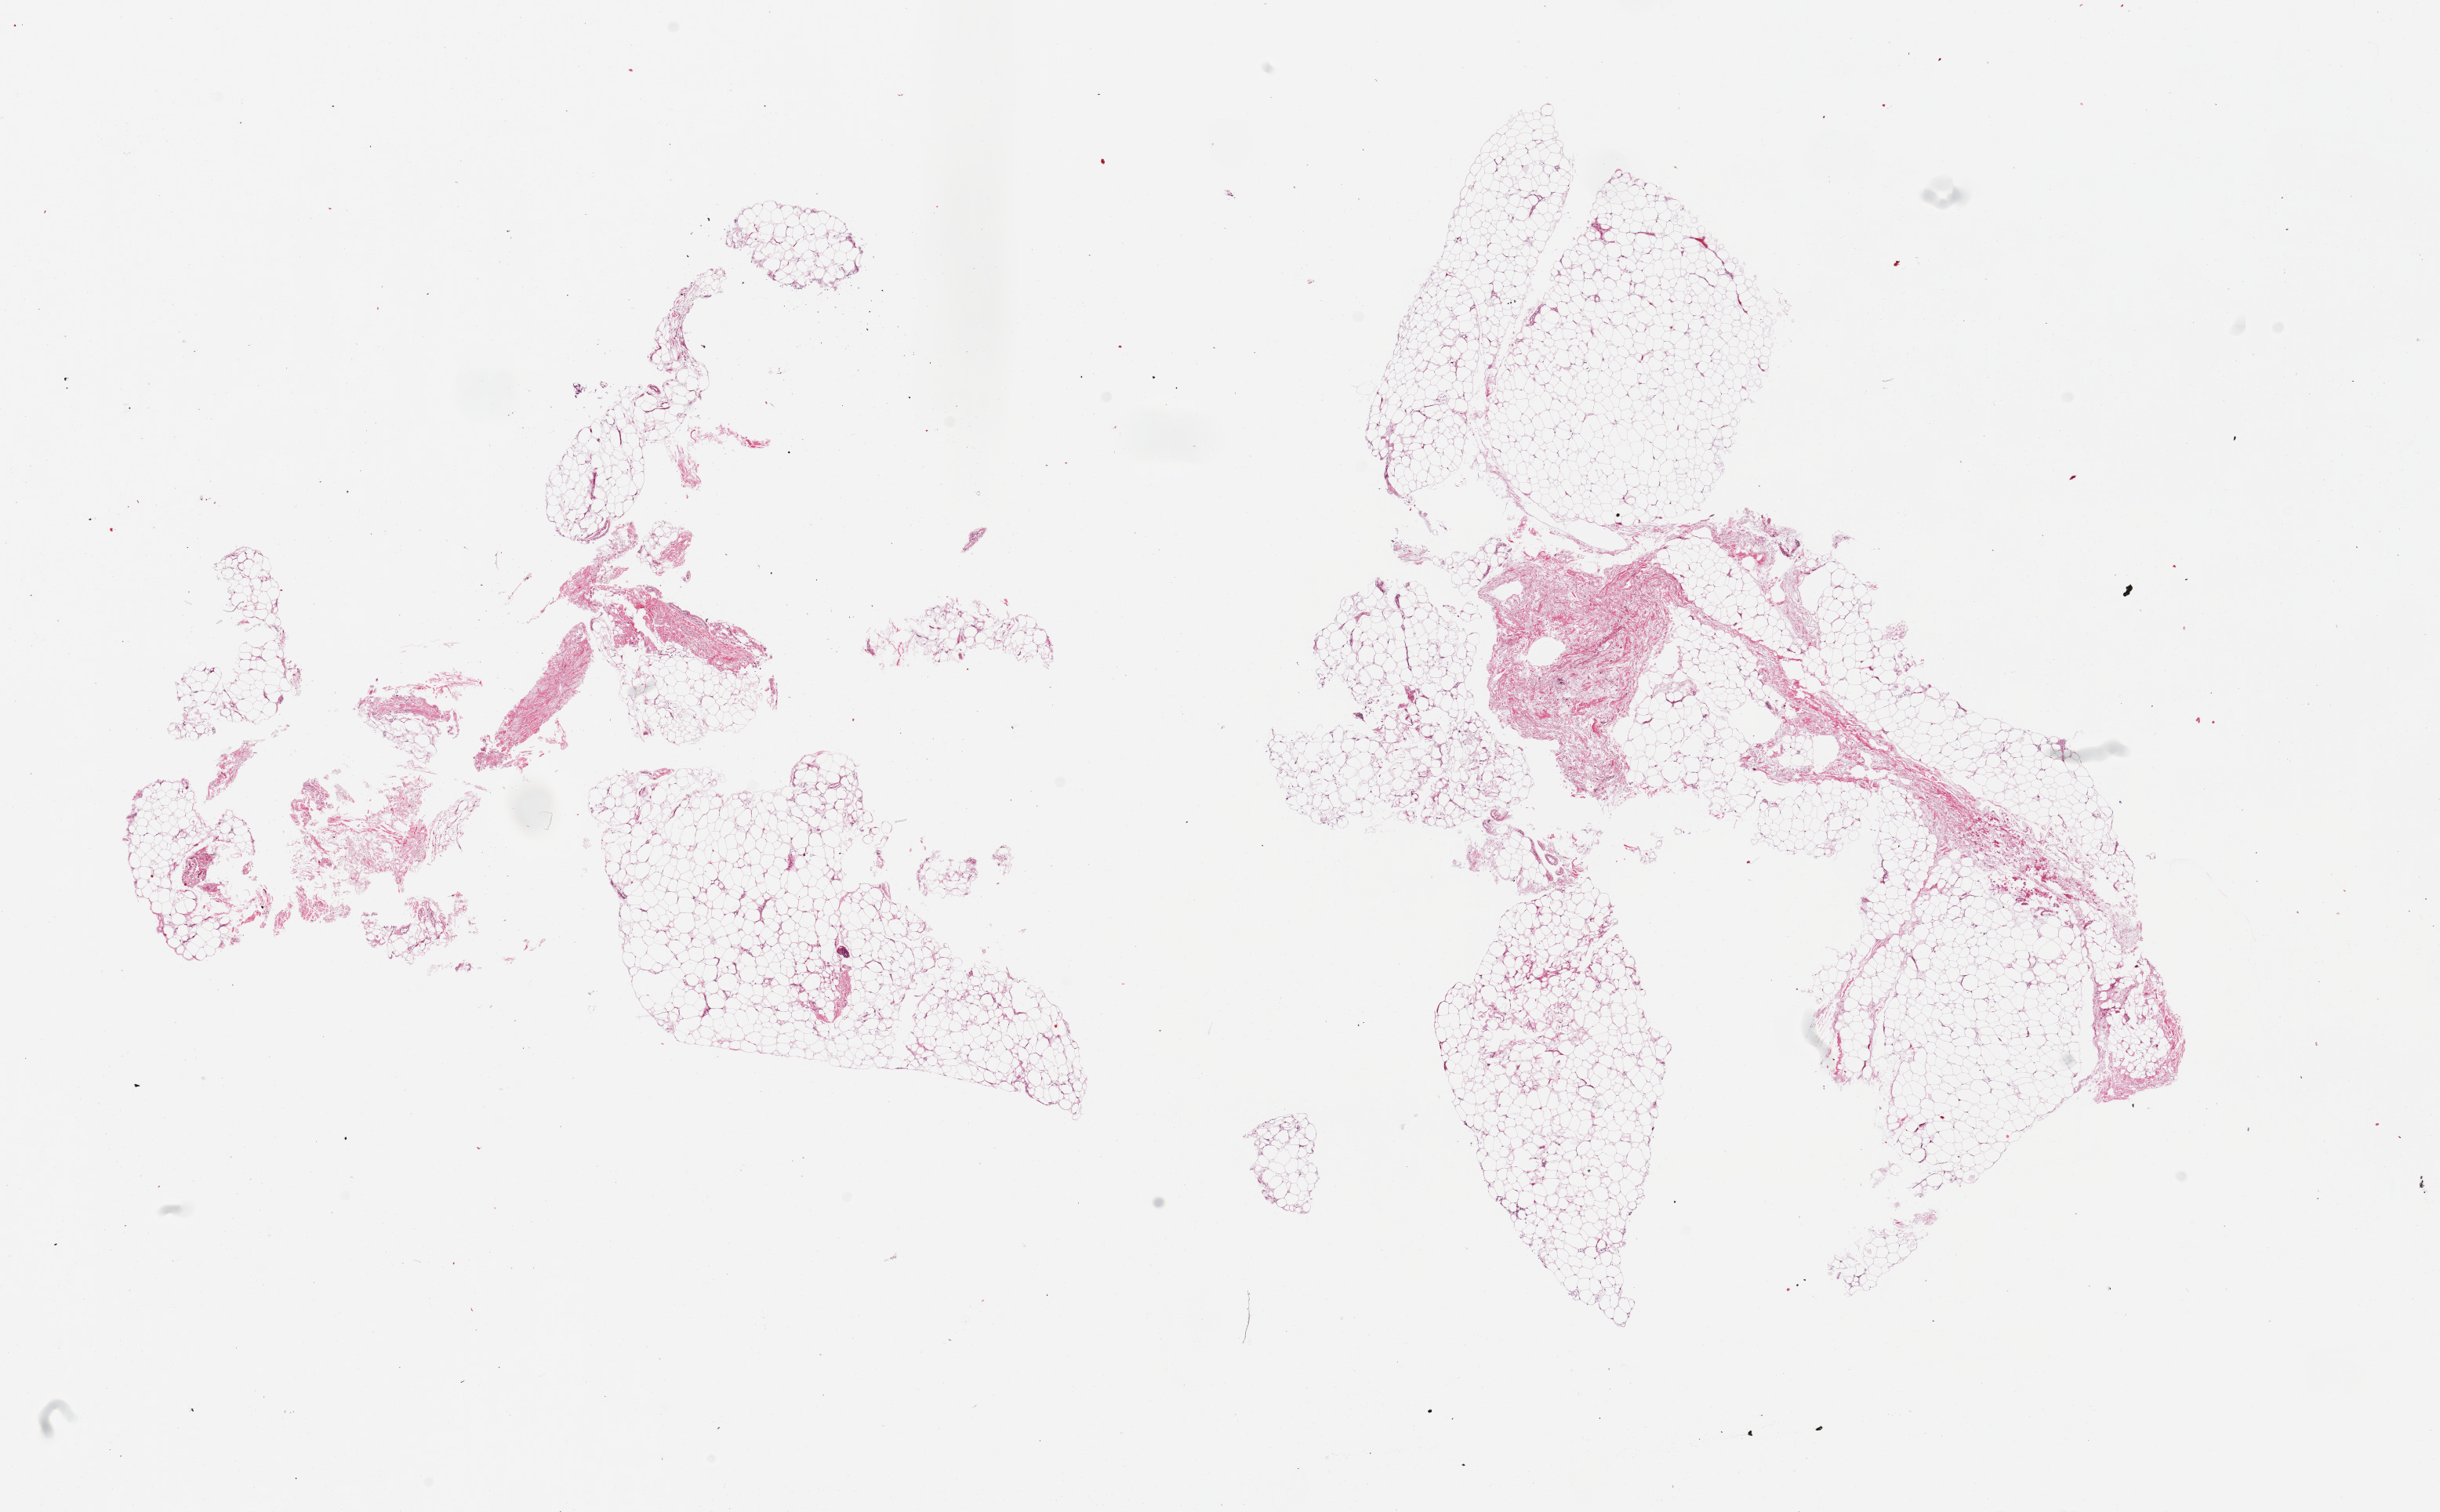
Digitized hematoxylin and eosin (H&E)-stained section — shown as a low-resolution overview of the whole scanned area (about 24.6 x 15.3 mm), PAXgene-fixed, paraffin-embedded tissue, sampled site (target tissue): adipose tissue, tissue donor sample. Female donor.
* review note (as recorded): 2 pieces; fat with 10 and 20% fibrovascular tissue